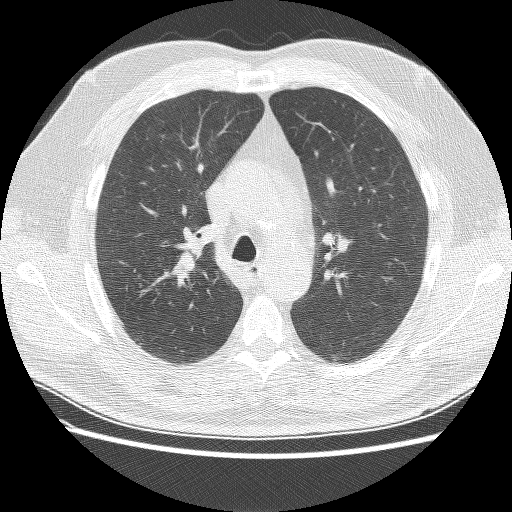
Low-dose screening chest CT, axial slice; baseline annual screen; lung window (W 1500 / L -600 HU); 2.5 mm slice thickness; lung (sharp) reconstruction kernel (BONE). Male participant, aged 57 years at enrolment. Current smoker at enrolment.
Expert reader's lesion annotation, bounding box [x1, y1, x2, y2] px = [156, 241, 212, 293]. No non-calcified nodule or mass ≥4 mm was recorded by the screening reader at this exam. Official screen result: negative screen, minor abnormalities not suspicious for lung cancer.